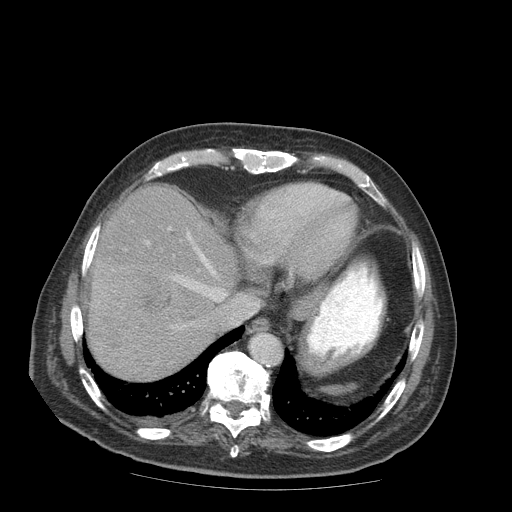
Contrast-enhanced abdominal CT (liver protocol), one axial slice. Position 75 of 99 along the scan axis. Reconstruction kernel STANDARD. Soft-tissue window (W 400 / L 40 HU). 2.5 mm slice thickness. 512 × 512 image matrix, field of view 420 × 420 mm. Case-level facts recorded for this patient, not image findings: diagnosis: hepatocellular carcinoma (patient treated with transarterial chemoembolisation; whether this scan precedes or follows treatment is not stated here); TNM stage (as recorded): Stage-IIIB; Child-Pugh class: A; tumour differentiation: well differentiated.
Annotated regions visible in this slice (semi-automatically segmented with operator editing):
- liver parenchyma outside the tumour (the mass and vessels are separate outlines, so this box may not span the whole liver): box from (x=88, y=185) to (x=236, y=378) px
- mass: (x=90, y=260)–(x=171, y=325)
- liver vessels: (x=146, y=228)–(x=216, y=330)